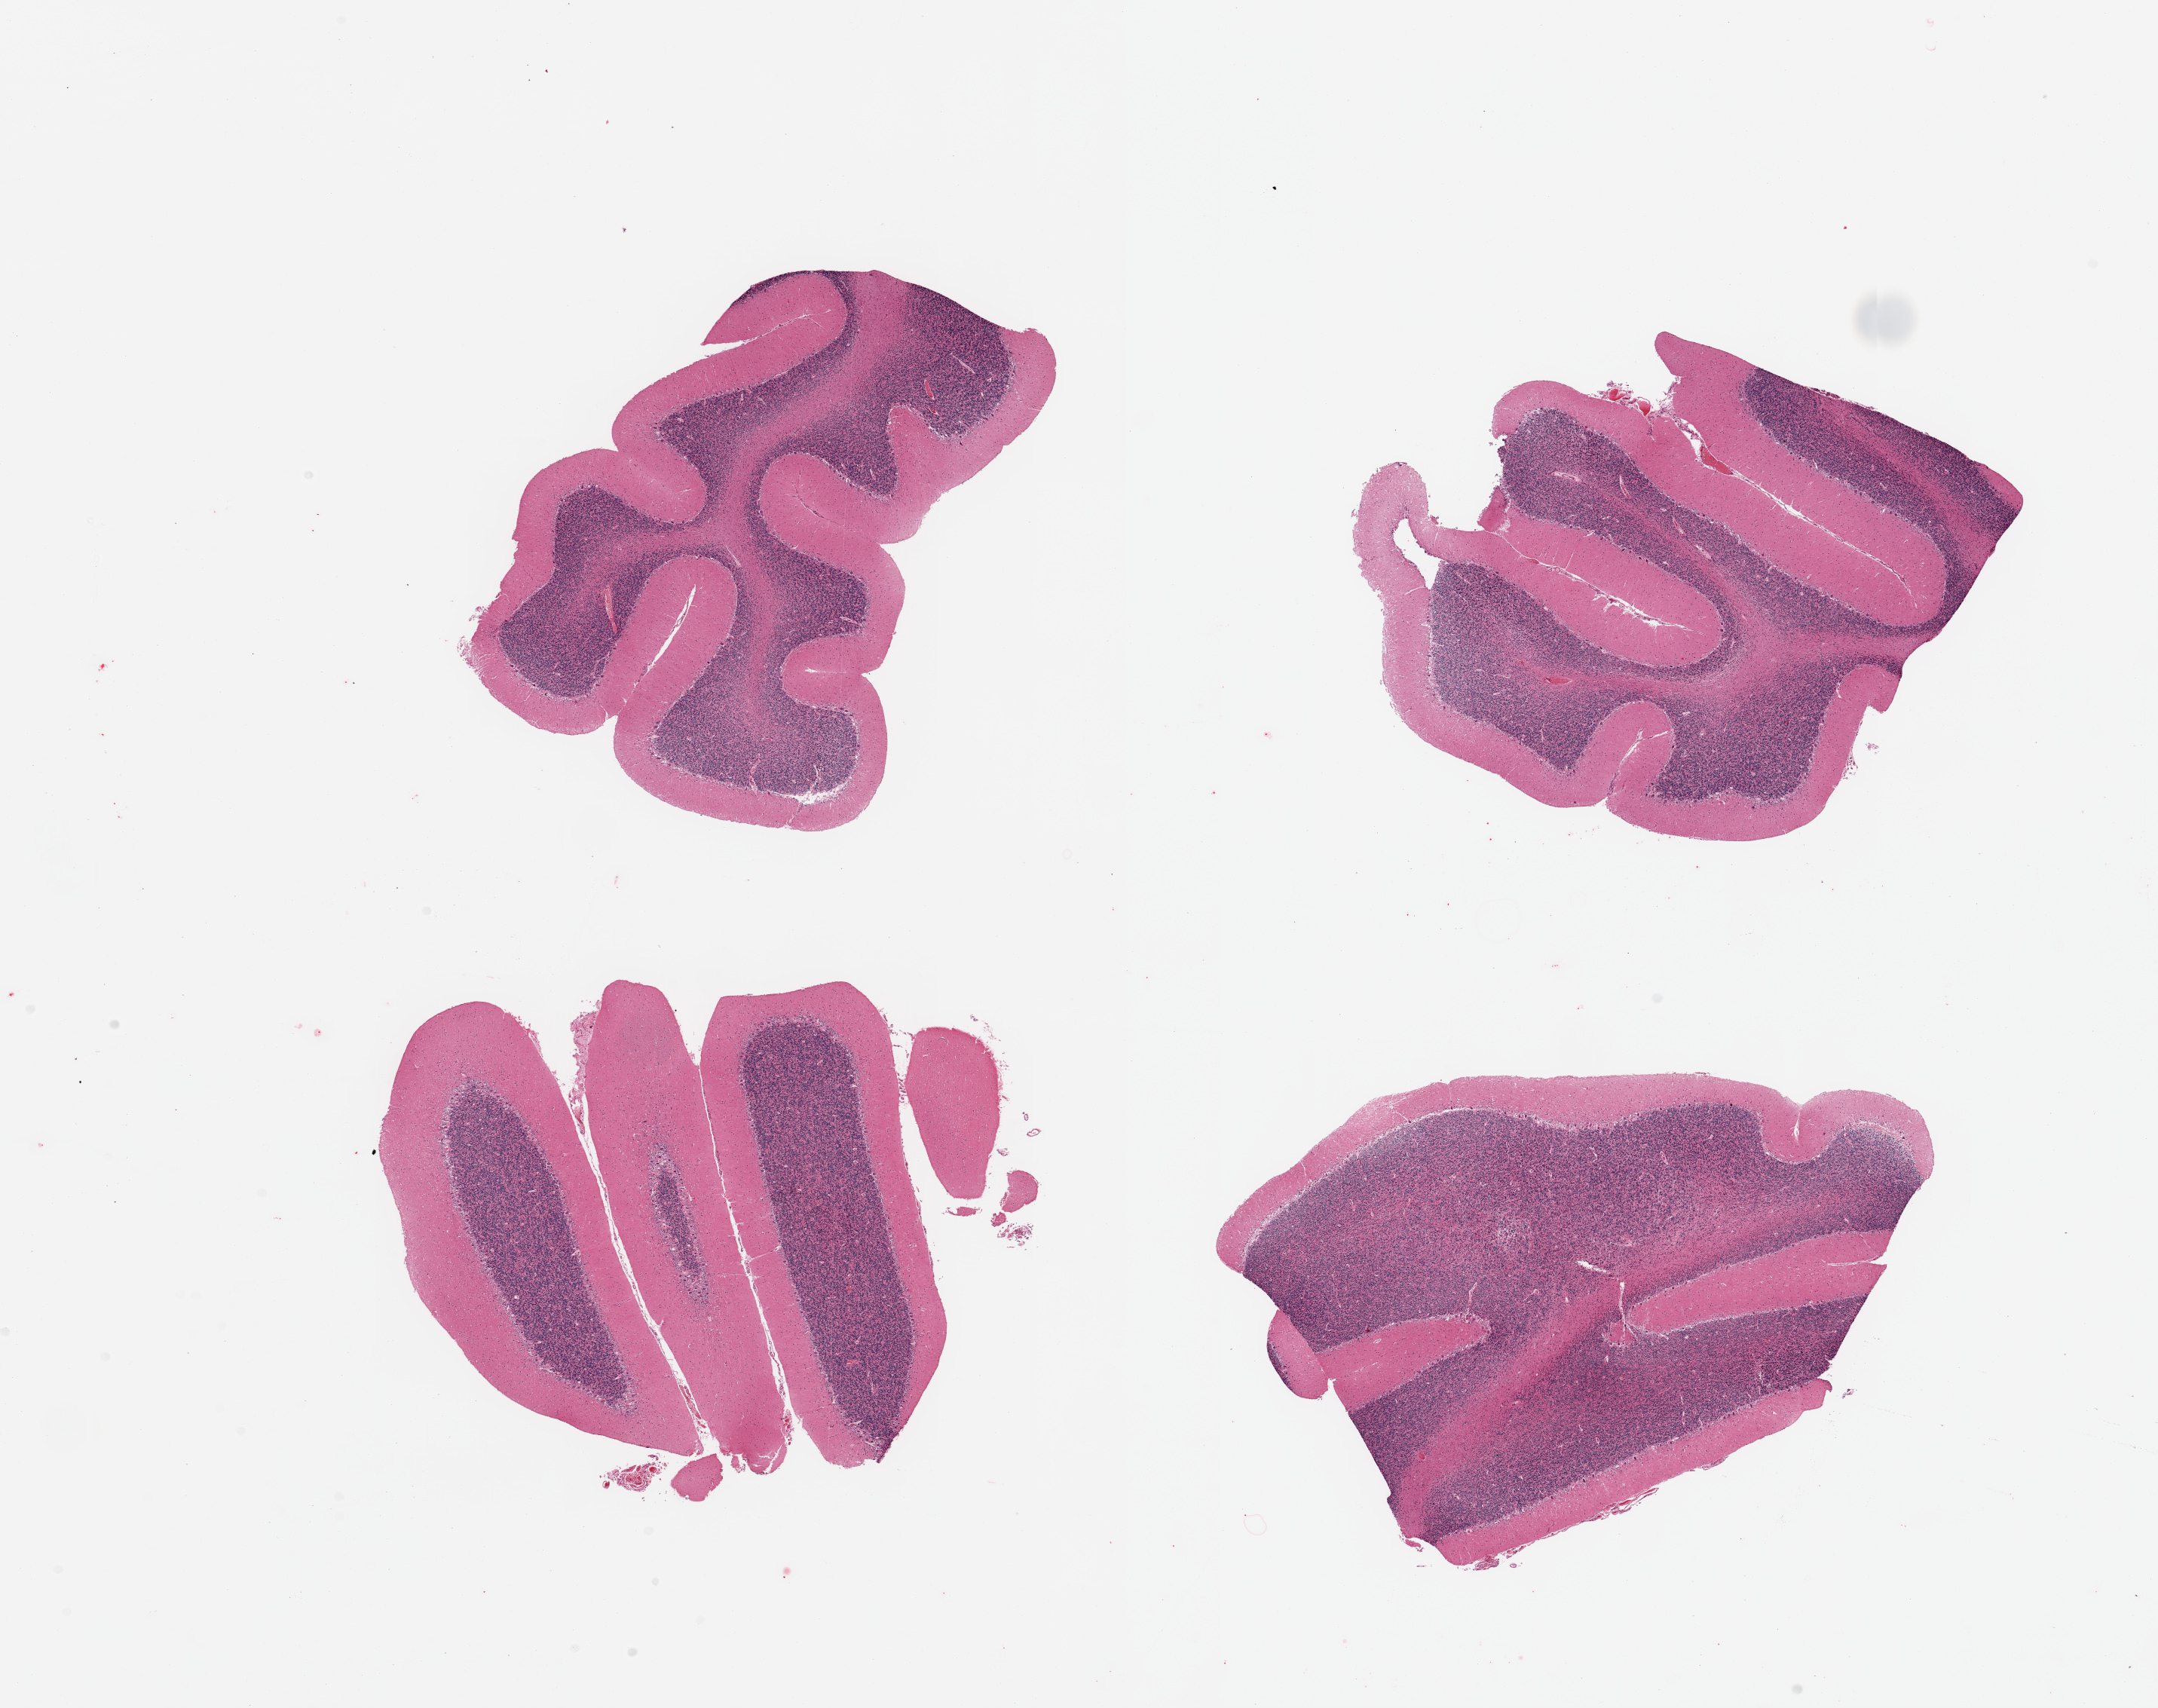
Whole-slide image, hematoxylin and eosin (H&E) stain — a low-resolution overview of the entire scanned area, about 22.6 x 17.9 mm. PAXgene-fixed, paraffin-embedded tissue. Section of cerebellum (target tissue). Donor tissue sample. Donor sex: male.
Pathologist's review note for this sample: 4 pieces.